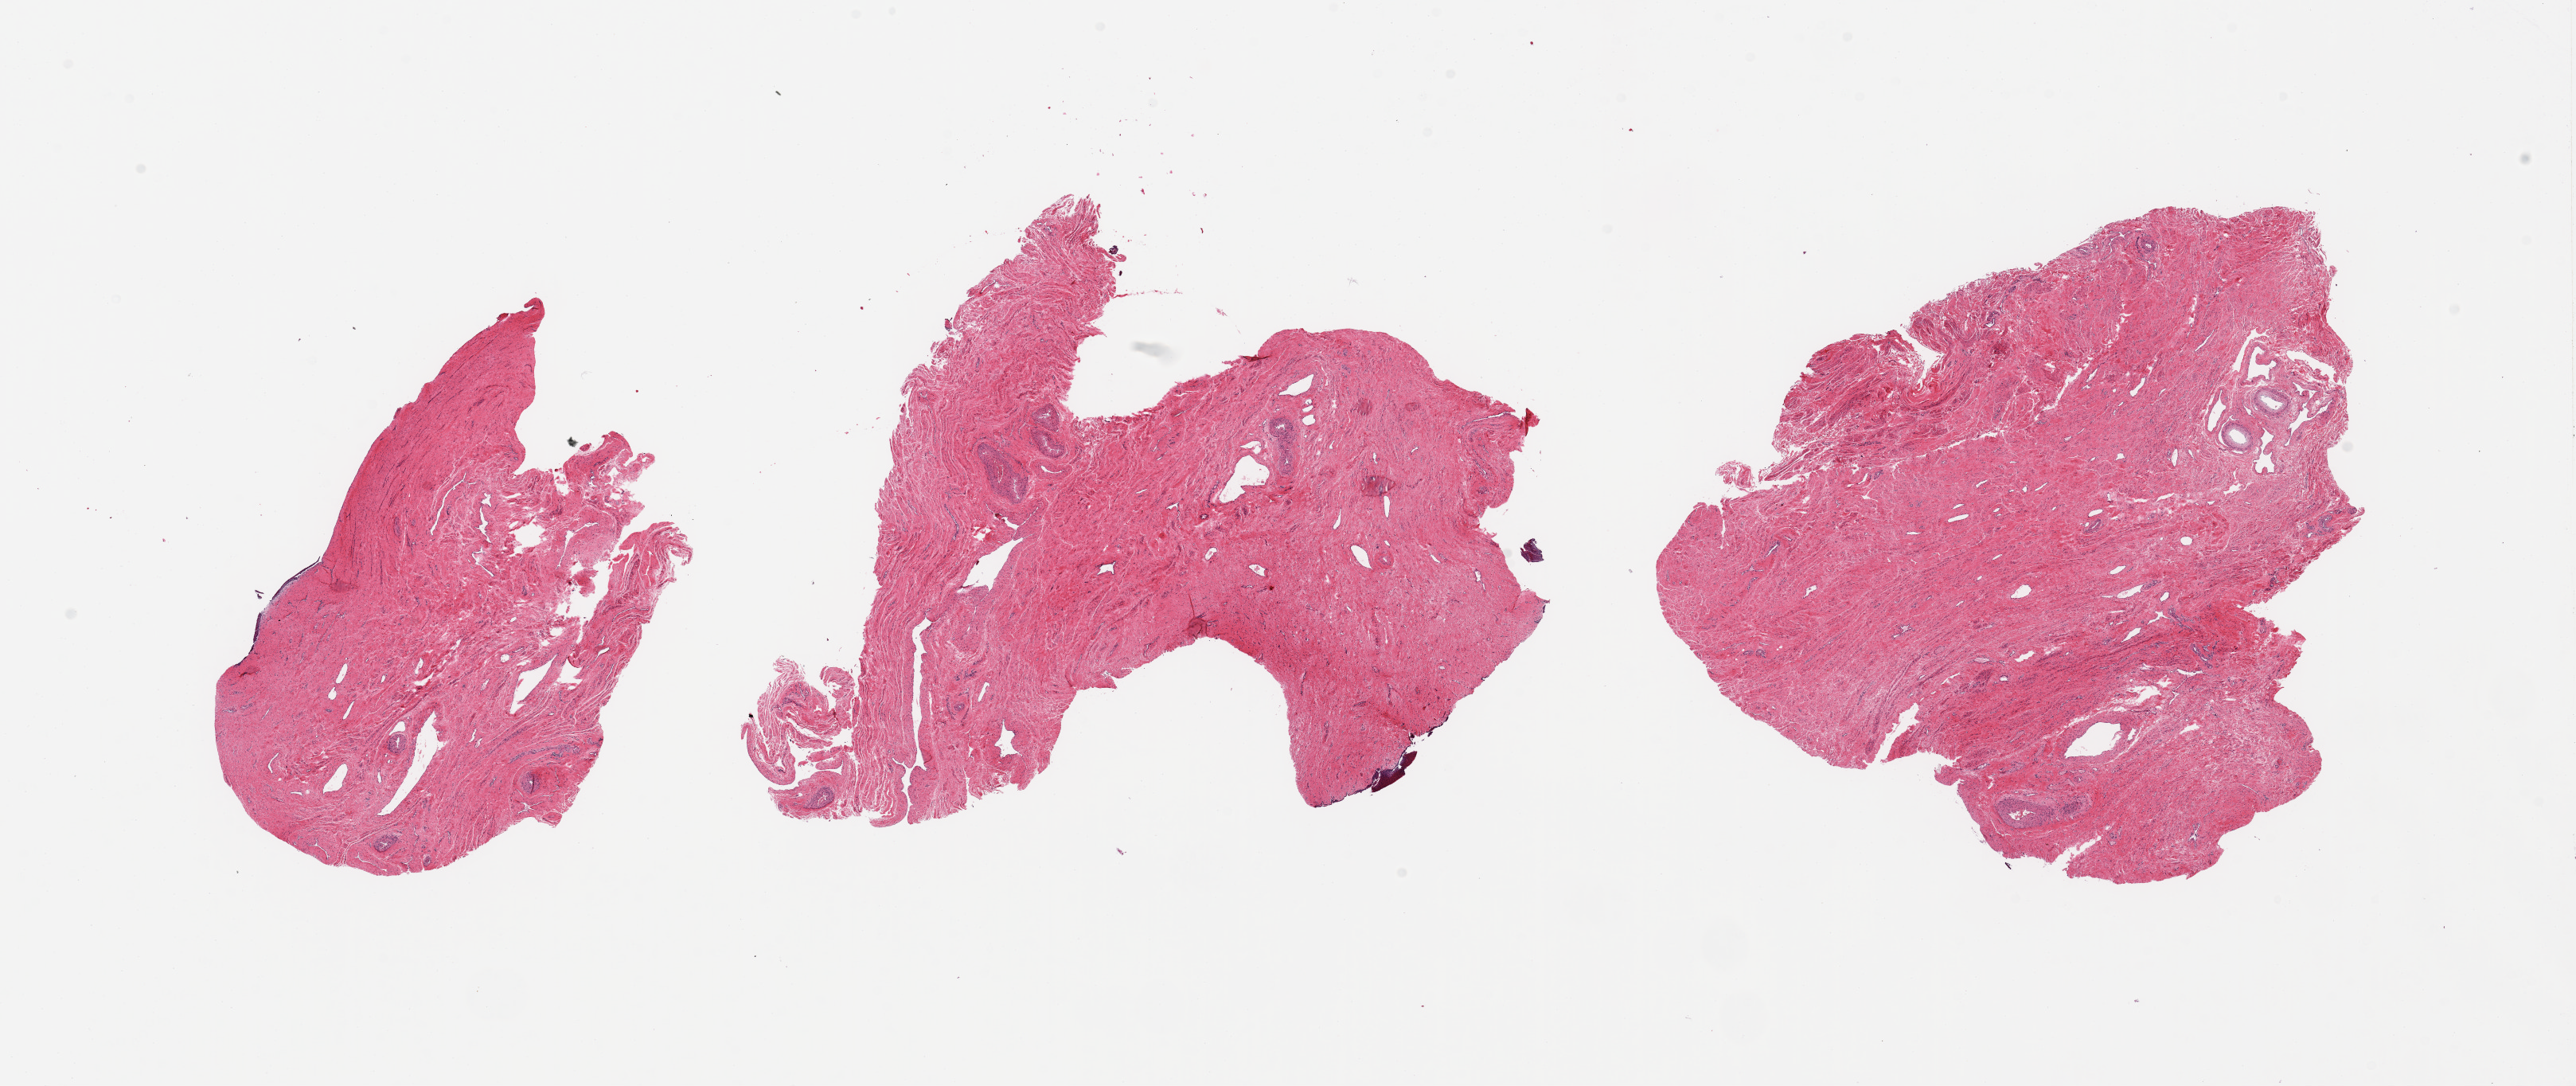
H&E whole-slide image, brightfield, a low-resolution overview of the entire scanned area, about 25.6 x 10.8 mm (acquisition: 20x scan), PAXgene-fixed, paraffin-embedded tissue, section of vagina (target tissue), tissue donor sample. Donor: female.
* pathologist's review note for this sample: 2 pieces, stromal/connective tissue, unknown provenance